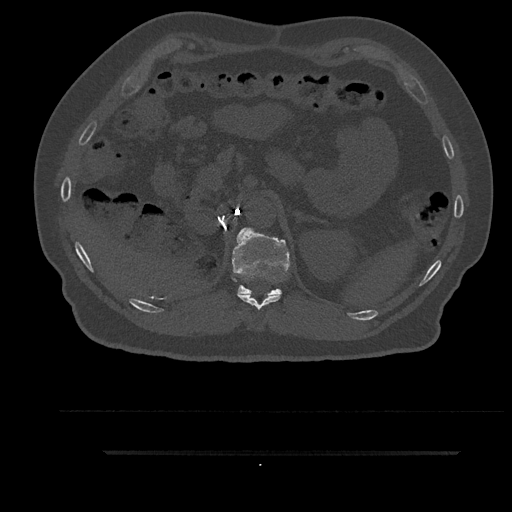
CT including the spine, one axial slice. Slice 271 of 797 in the series (ordered by position). Reconstruction kernel Br40s/3. 120 kVp. Bone window (W 1800 / L 400 HU). 512 × 512 image matrix. Patient: male, 63 years. Case-level facts recorded for this patient, not image findings: primary cancer: renal; vertebrae with lytic lesions (as recorded): T8.
Annotated regions visible in this slice (semi-automatically segmented with operator editing):
- T11 vertebra: box from (x=238, y=294) to (x=281, y=310) px
- T12 vertebra: (x=232, y=228)–(x=290, y=296)